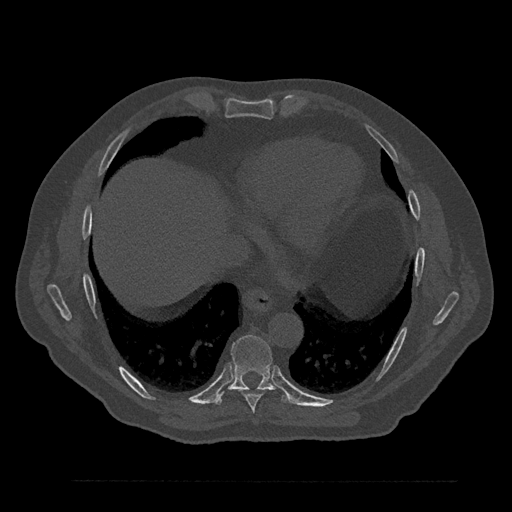
CT including the spine, one axial slice. Position 428 of 797 along the scan axis. 120 kVp. Bone window (W 1800 / L 400 HU). 0.5 mm slice thickness. 512 × 512 image matrix, field of view 430 × 430 mm. Patient: male, 61 years. Case-level facts recorded for this patient, not image findings: primary cancer: prostate.
Outlined on this slice (semi-automatically segmented with operator editing):
- T8 vertebra: bounding box [x1, y1, x2, y2] px = [237, 389, 264, 413]
- T9 vertebra: [214, 335, 292, 406]